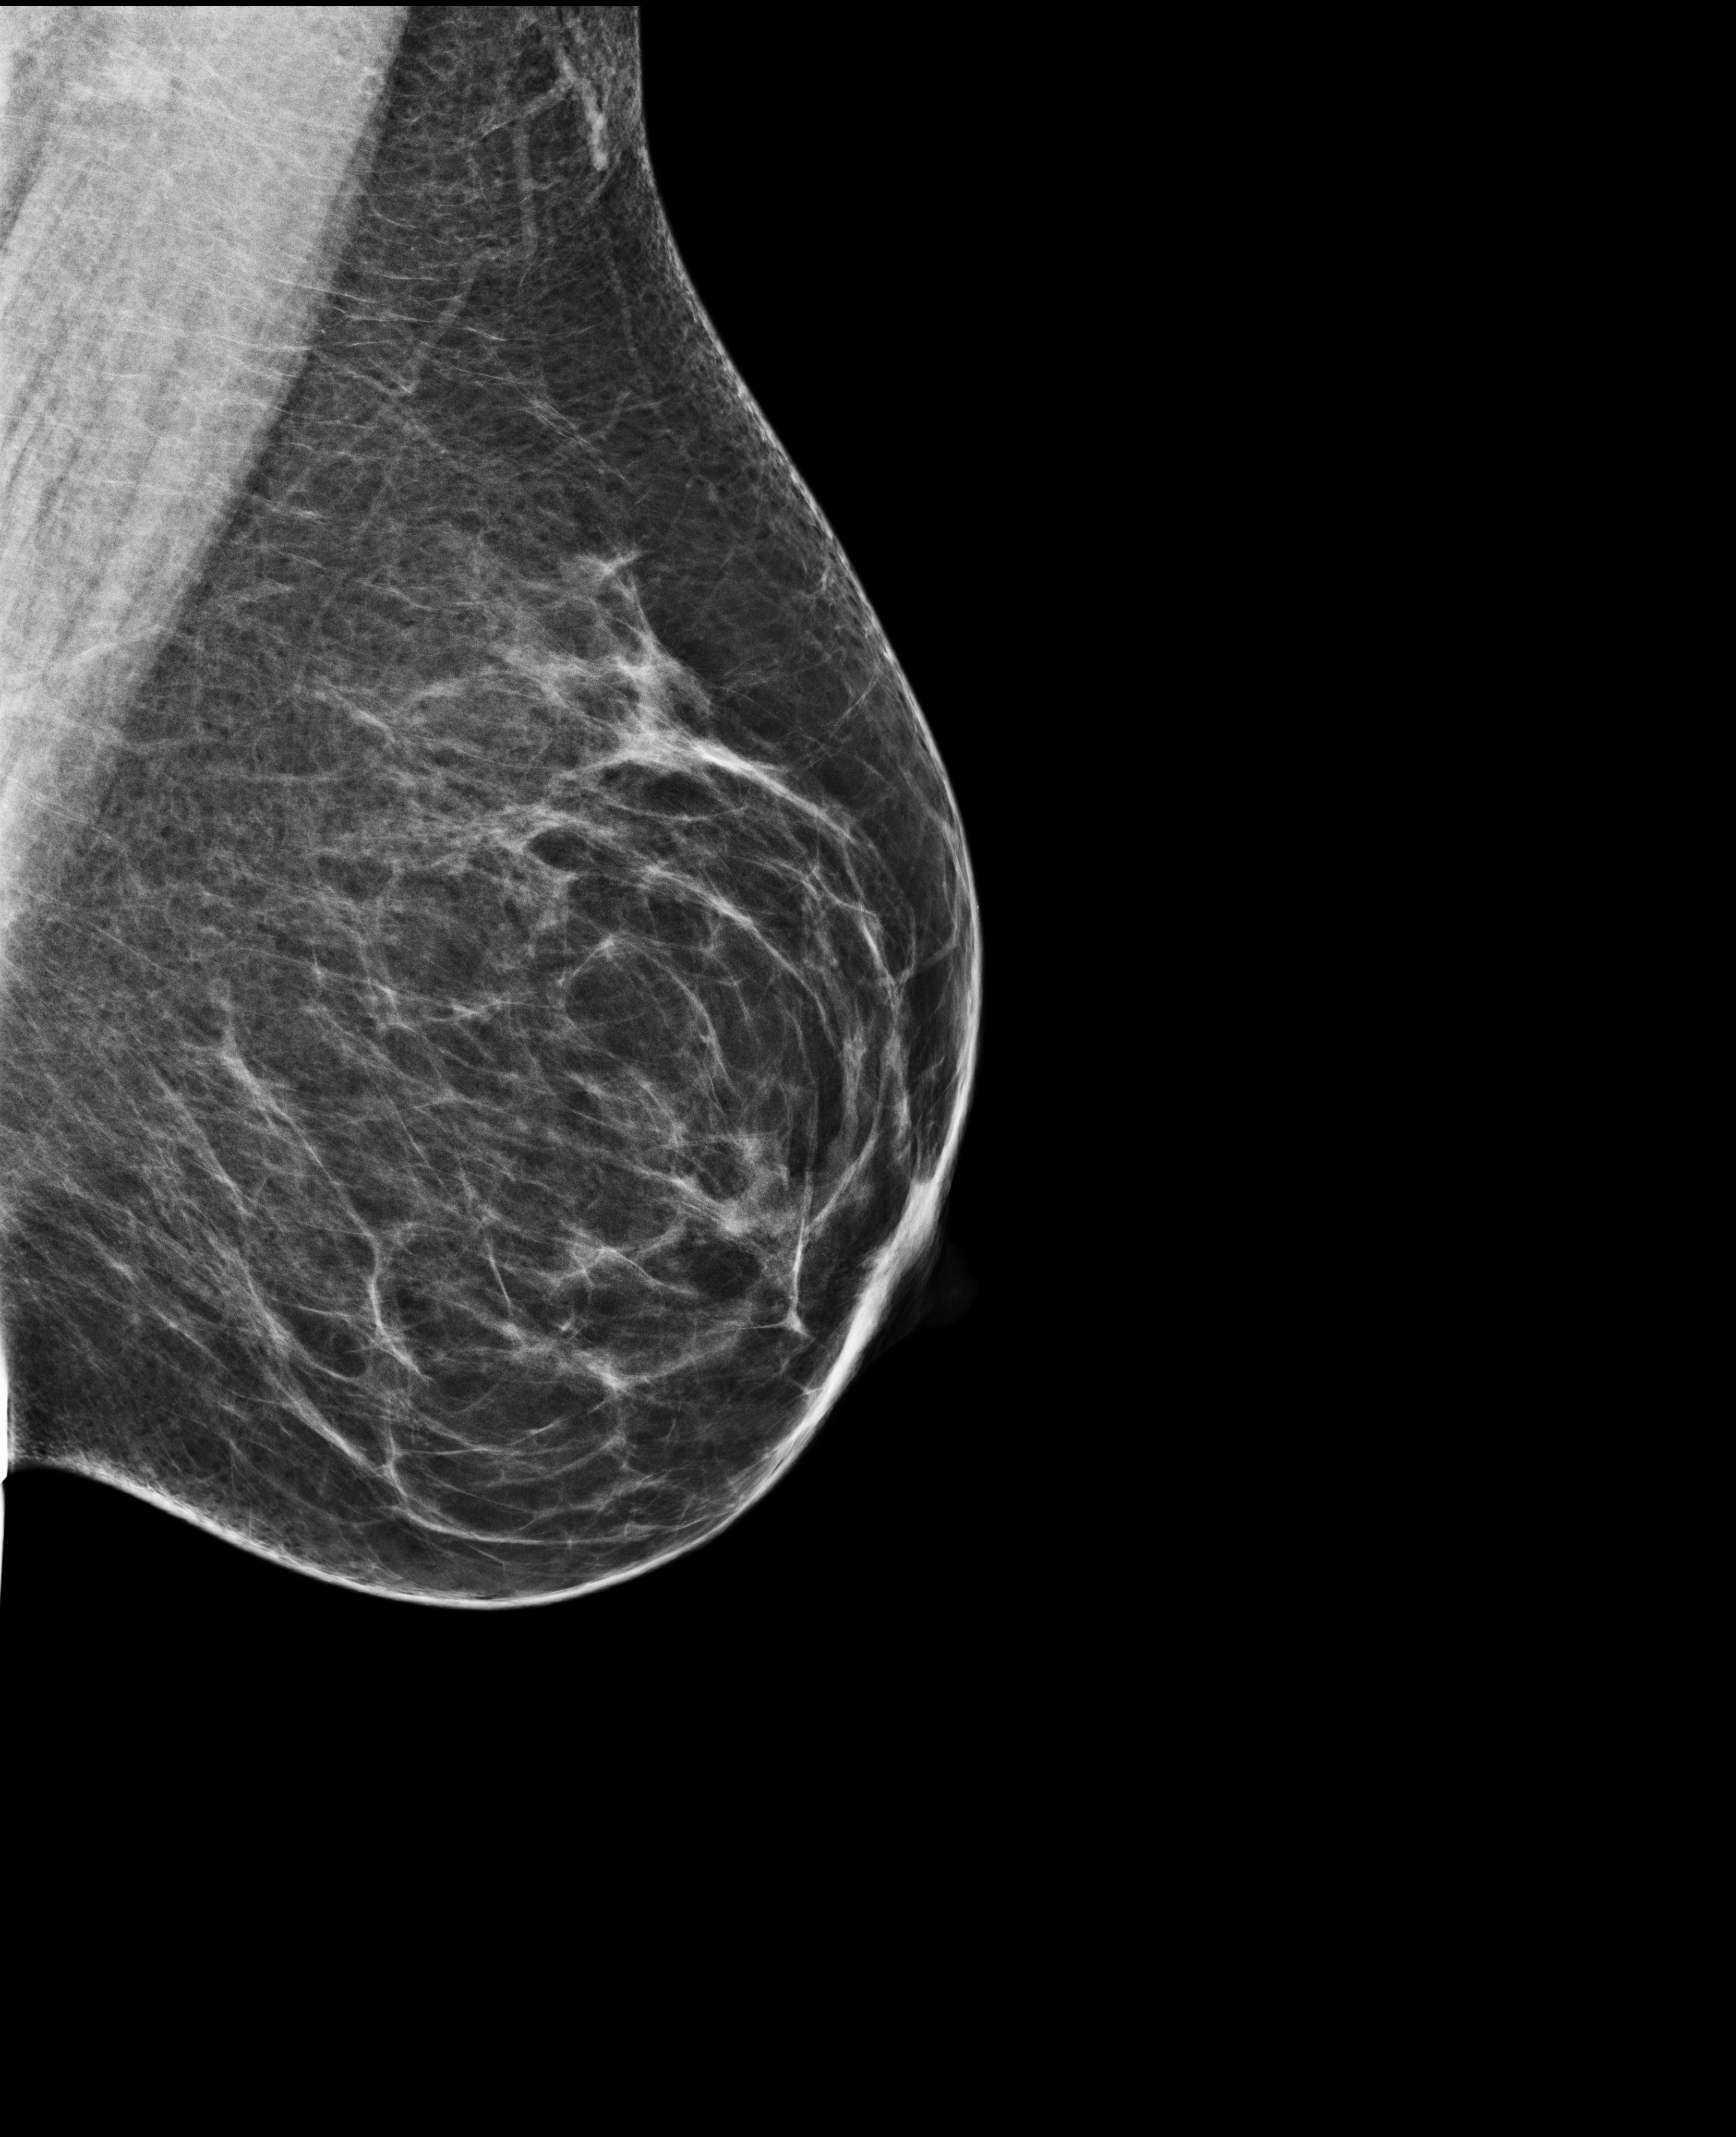
Digital mammogram (FFDM), left breast, mediolateral oblique (MLO) view, screening examination. Female patient, age 41 years.
BI-RADS breast density category at the screening exam (both breasts, scale 1–4): 3. Final BI-RADS assessment for this screening round (tomosynthesis exam, both breasts): category 1. Recall: no recall after this screen.